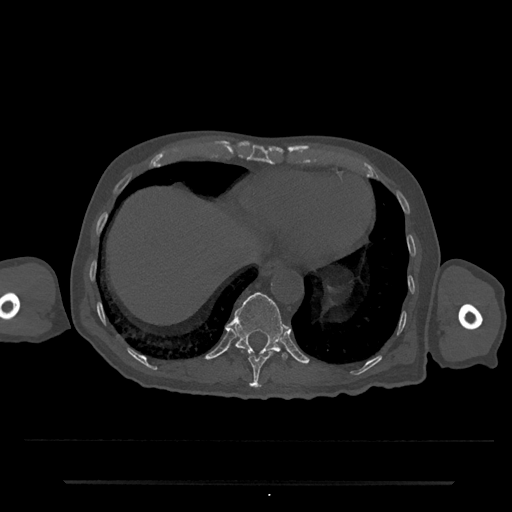
CT including the spine, one axial slice. Position 280 of 797 along the scan axis. 120 kVp. Bone window (W 1800 / L 400 HU). 512 × 512 image matrix, field of view 427 × 427 mm. Male patient, age 74 years. Case-level facts recorded for this patient, not image findings: primary cancer: prostate.
Annotated regions visible in this slice (semi-automatically segmented with operator editing):
- T10 vertebra: box from (x=242, y=350) to (x=276, y=388) px
- T11 vertebra: (x=227, y=292)–(x=288, y=360)